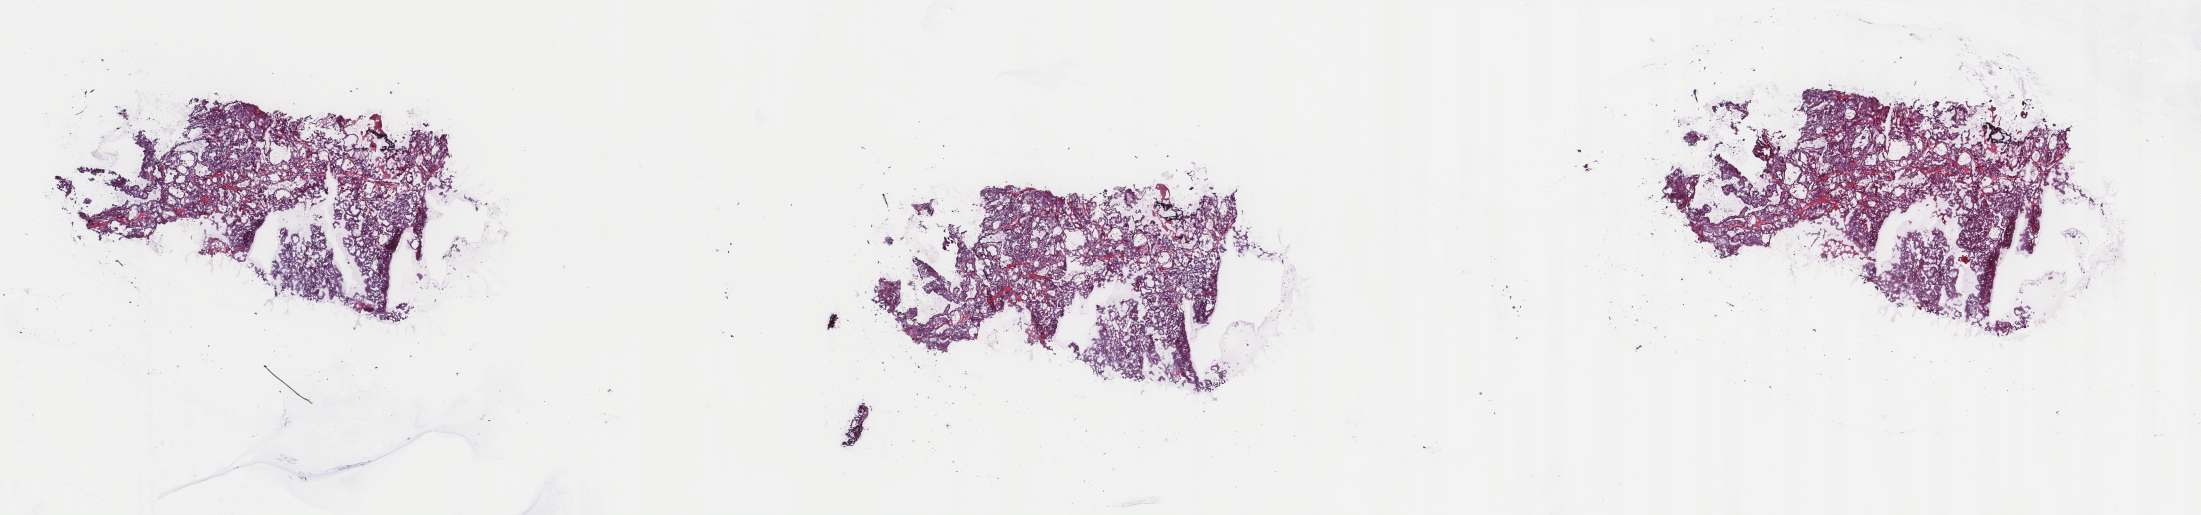
Hematoxylin and eosin (H&E) stained whole-slide image — low-resolution overview of the scanned area, about 34.9 x 8.2 mm. Frozen section from the top of the tissue portion. Sample: primary tumour, thyroid. Female, age 65 years at initial diagnosis. Slide review estimates, as recorded: tumour cells 90%, tumour nuclei 100%, normal cells 0%, stromal cells 10%, necrosis 0%. Inflammatory infiltration, as recorded: lymphocyte infiltration 0%, monocyte infiltration 2%, neutrophil infiltration 0%.
* AJCC pathologic stage: III (6th edition)
* pathologic diagnosis: Papillary adenocarcinoma, NOS